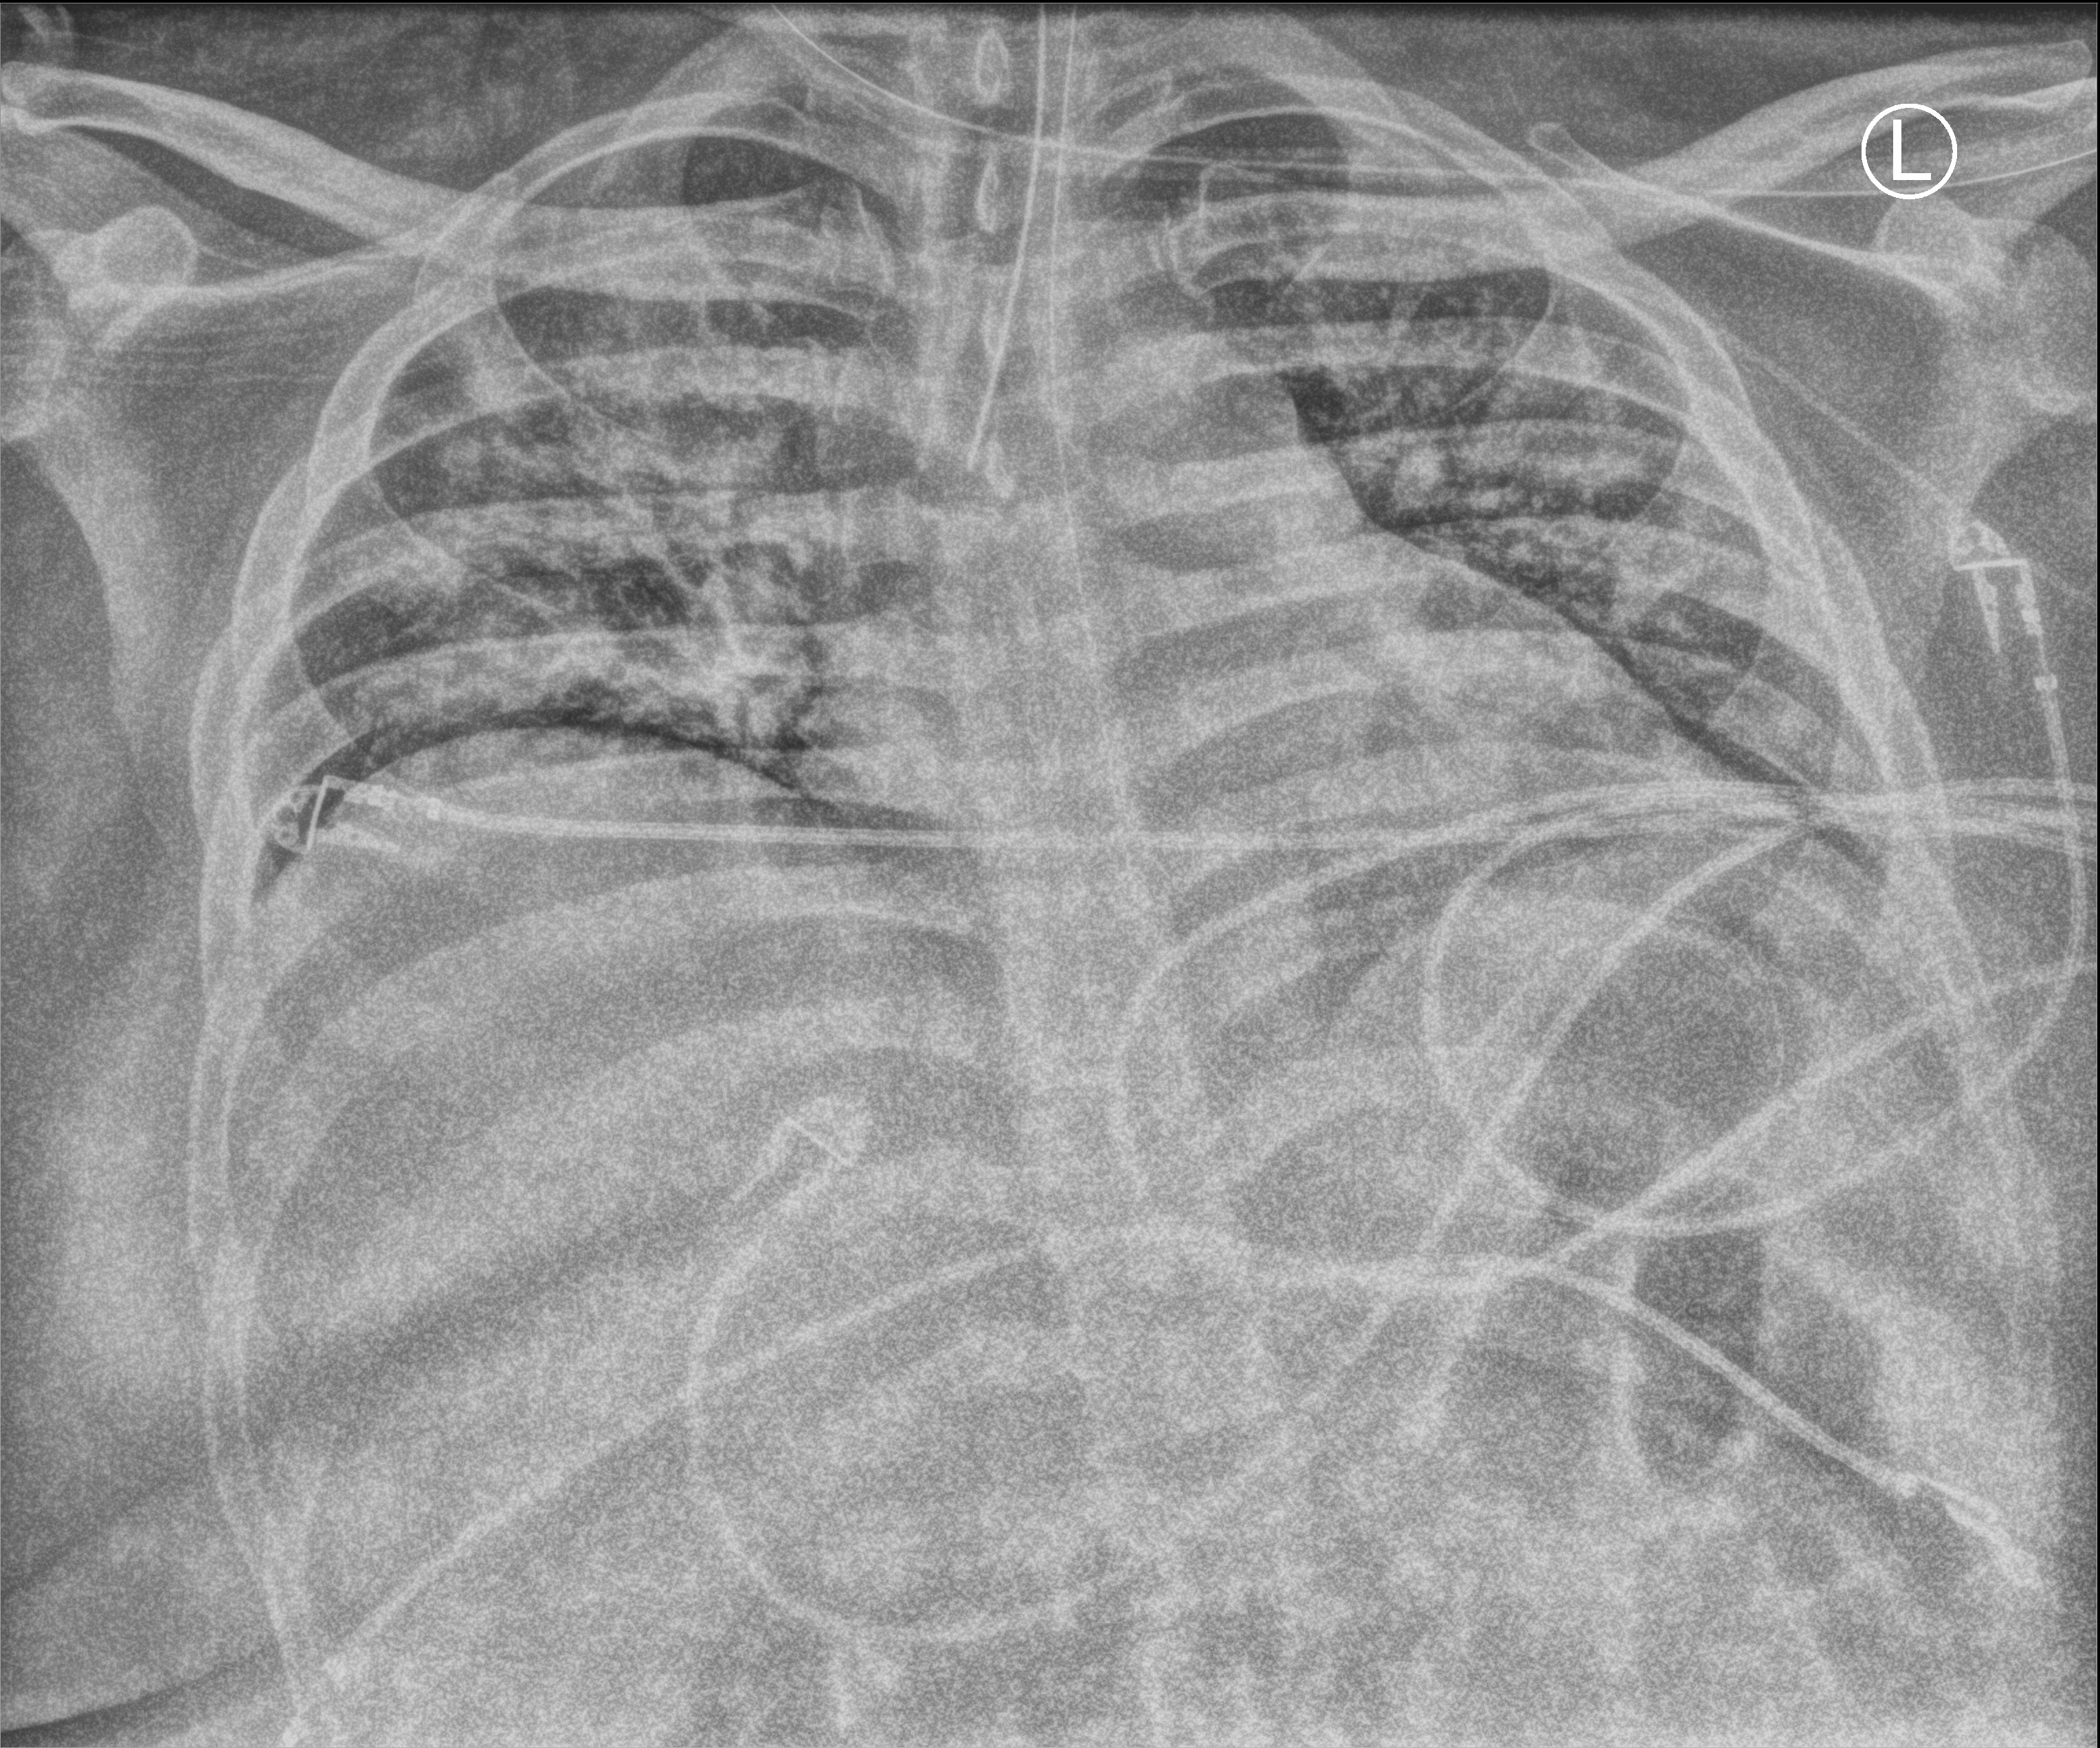
Portable chest radiograph. Patient hospitalised with COVID-19; male, aged 18–59 years.
From the hospital-stay record, not from the radiograph (when in the stay this image was taken is not recorded):
- admitted to intensive care during this hospital stay: yes
- hypertension (admission record): no
- mechanically ventilated during this hospital stay: yes